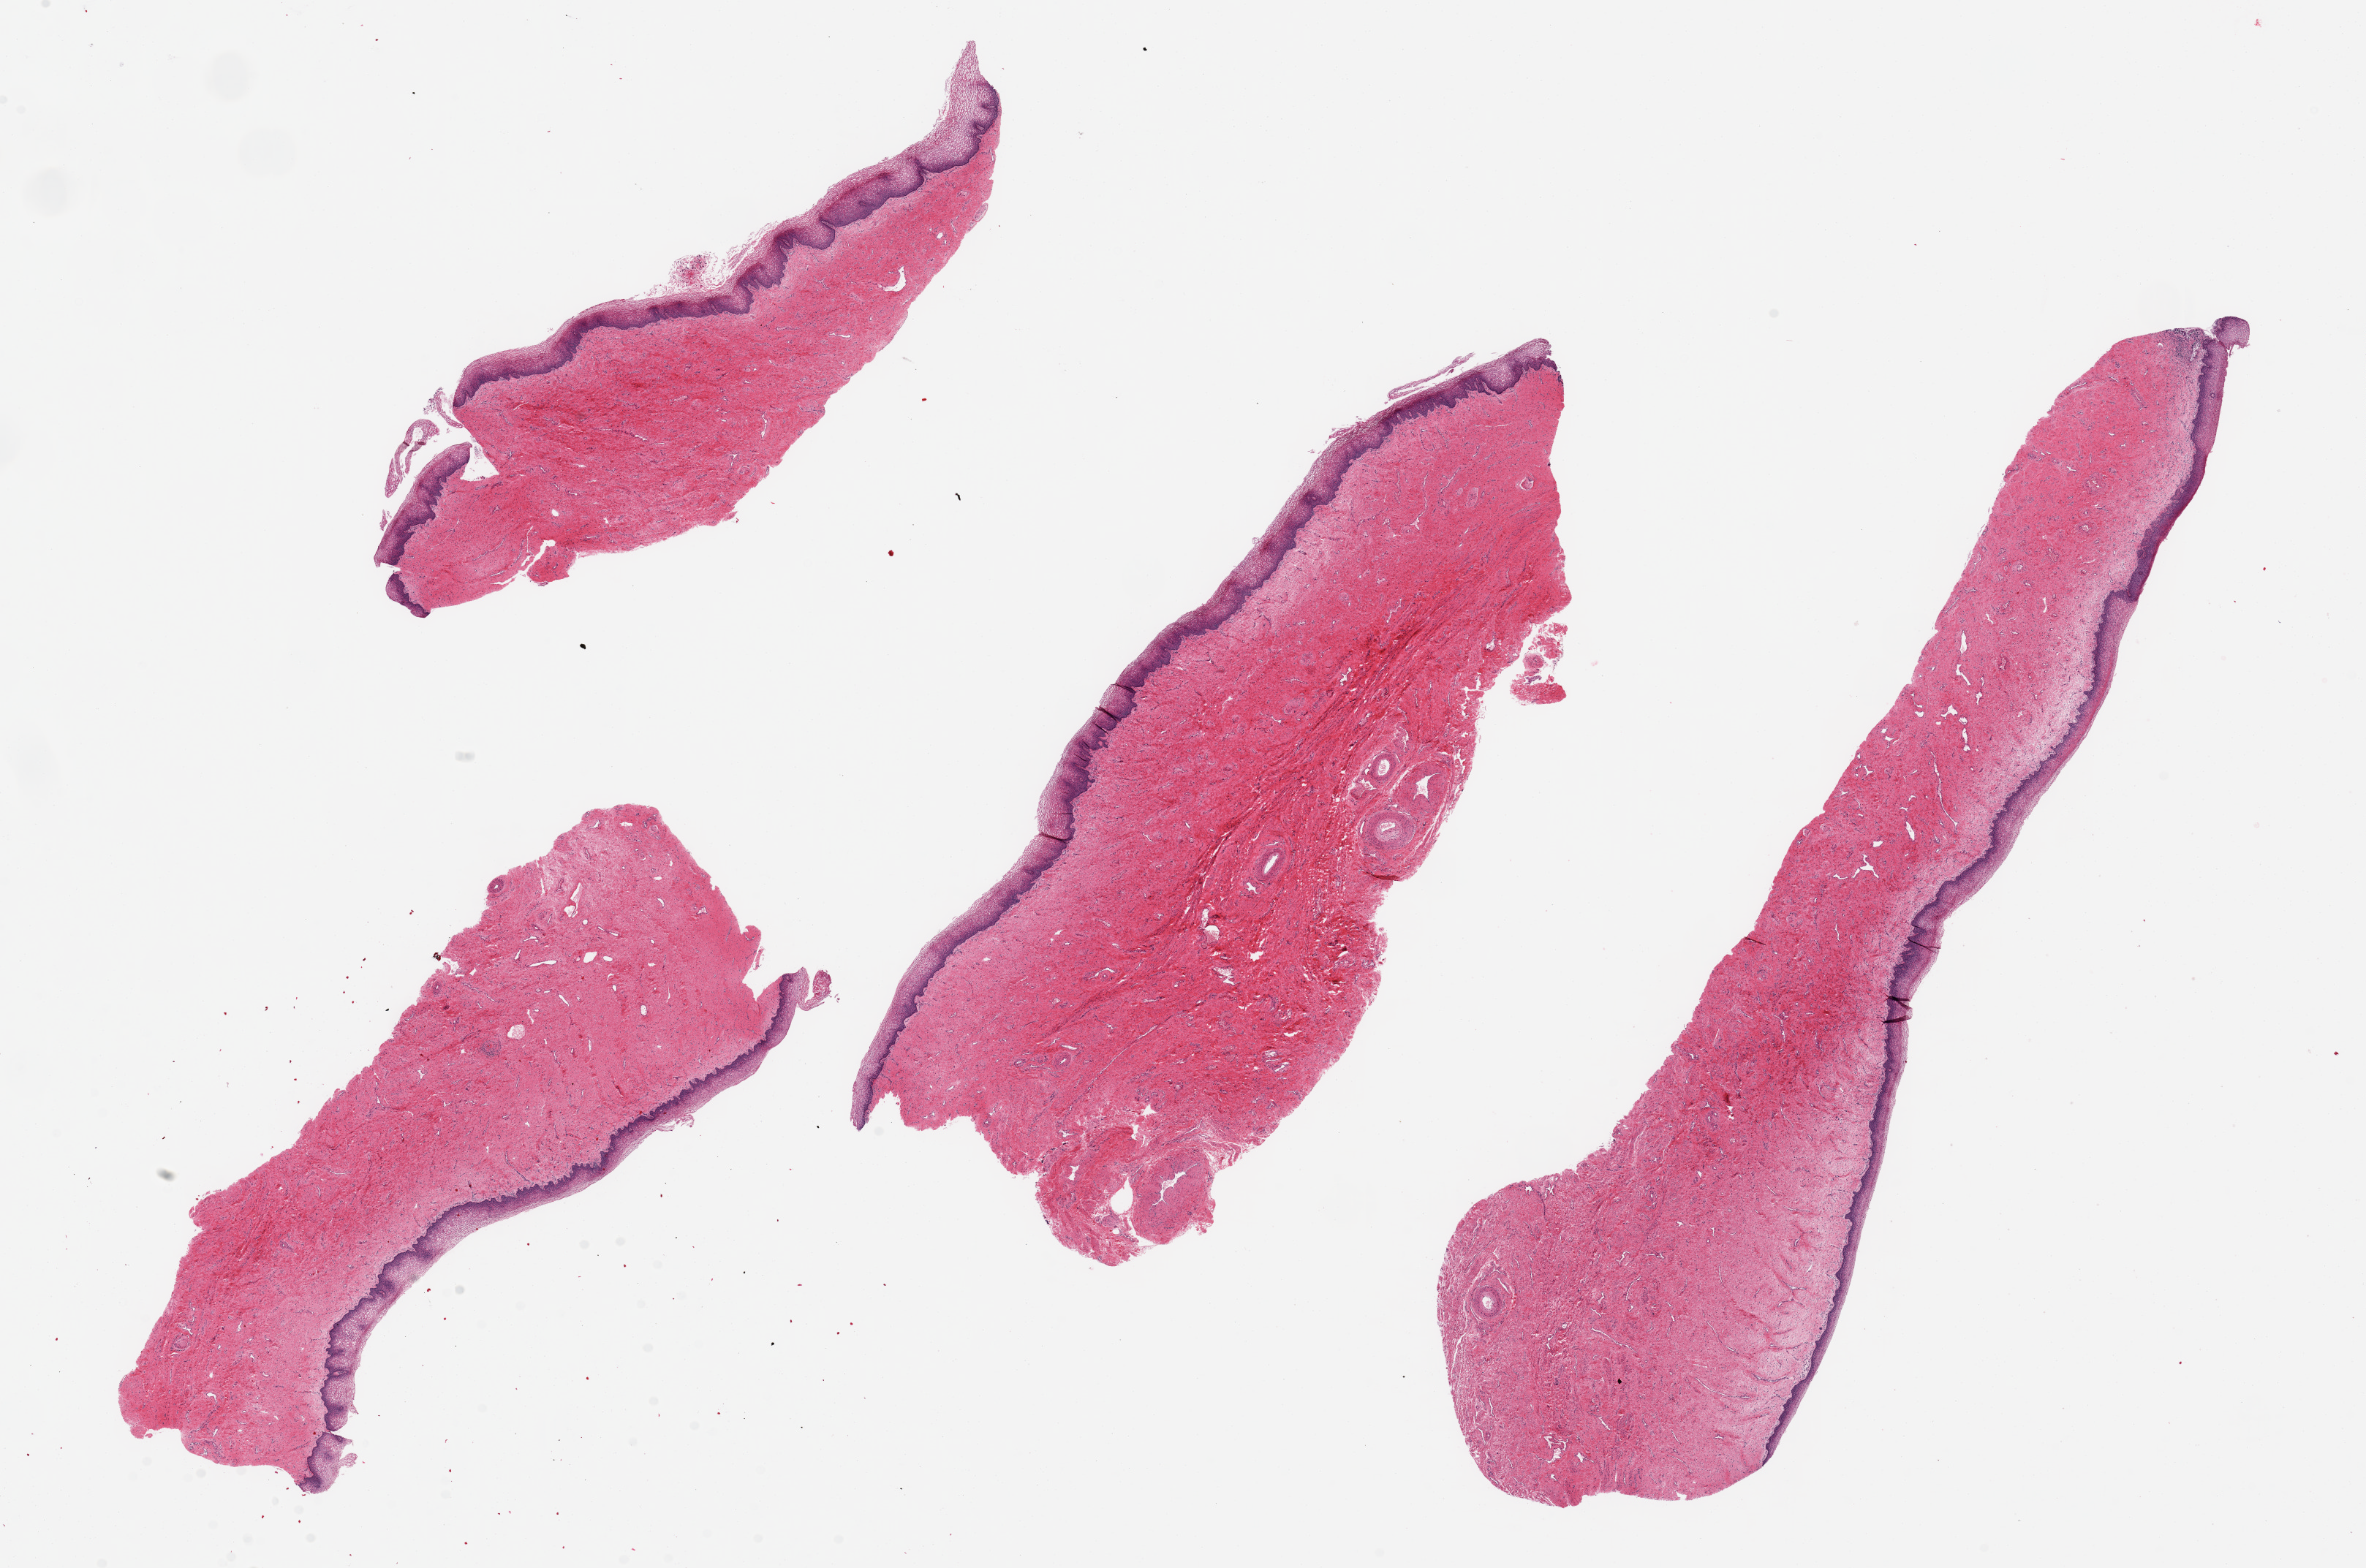
H&E whole-slide image — low-resolution overview of the scanned area, about 25.6 x 17.0 mm (acquisition: 20x scan), PAXgene-fixed, paraffin-embedded tissue, section of exocervix (target tissue), donor tissue sample. Female donor.
Reviewer comment on this tissue sample: 4 pieces, up to 13.6x3.6 mm; ENDOCERVIX with abundant glands.